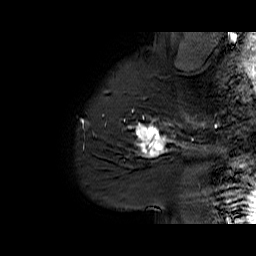
Breast MRI (dynamic contrast-enhanced), one sagittal slice. Slice 51 of 60 in the series (ordered by position). Dynamic contrast-enhanced series, time point 2 of 6 at this slice position (early post-contrast). 1.5 T. TE 6.1 ms, TR 32.9 ms. 256 × 256 image matrix, field of view 220 × 220 mm. Female patient. Case-level facts recorded for this patient, not image findings: setting: breast cancer imaged before/during neoadjuvant chemotherapy; receptor status: HER2-positive.
Outlined on this slice (semi-automatically segmented with operator editing):
- analysis volume of interest (the breast-tissue region the enhancement analysis was run in; not a lesion): bounding box <127,95,194,165> (left, top, right, bottom; pixels)
- tumour enhancement mask (voxels above the 100 % enhancement threshold inside the analysis volume of interest): <135,115,194,157>